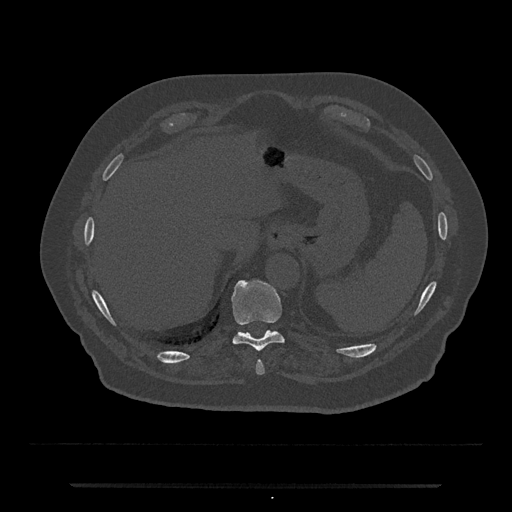
CT including the spine, one axial slice. Position 703 of 797 along the scan axis. Reconstruction kernel Br40s/3. 120 kVp. Bone window (W 1800 / L 400 HU). 0.5 mm slice thickness. 512 × 512 image matrix, field of view 434 × 434 mm. Patient: male, 80 years. From the clinical record (not read from this slice): primary cancer: prostate.
Structures marked on this image (semi-automatically segmented with operator editing):
- T10 vertebra: box from (x=231, y=280) to (x=284, y=352) px
- T9 vertebra: (x=256, y=360)–(x=265, y=375)